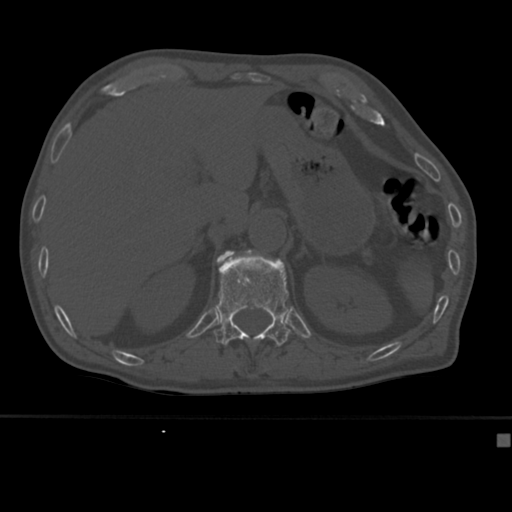
CT including the spine, one axial slice; position 191 of 430 along the scan axis; reconstruction kernel Br40s; 120 kVp; bone window (W 1800 / L 400 HU); 512 × 512 image matrix, field of view 337 × 337 mm. Male patient, age 64 years. Case-level facts recorded for this patient, not image findings: primary cancer: uterus.
Outlined on this slice (semi-automatically segmented with operator editing):
- L1 vertebra: box from (x=216, y=251) to (x=235, y=265) px
- T12 vertebra: (x=214, y=250)–(x=291, y=346)